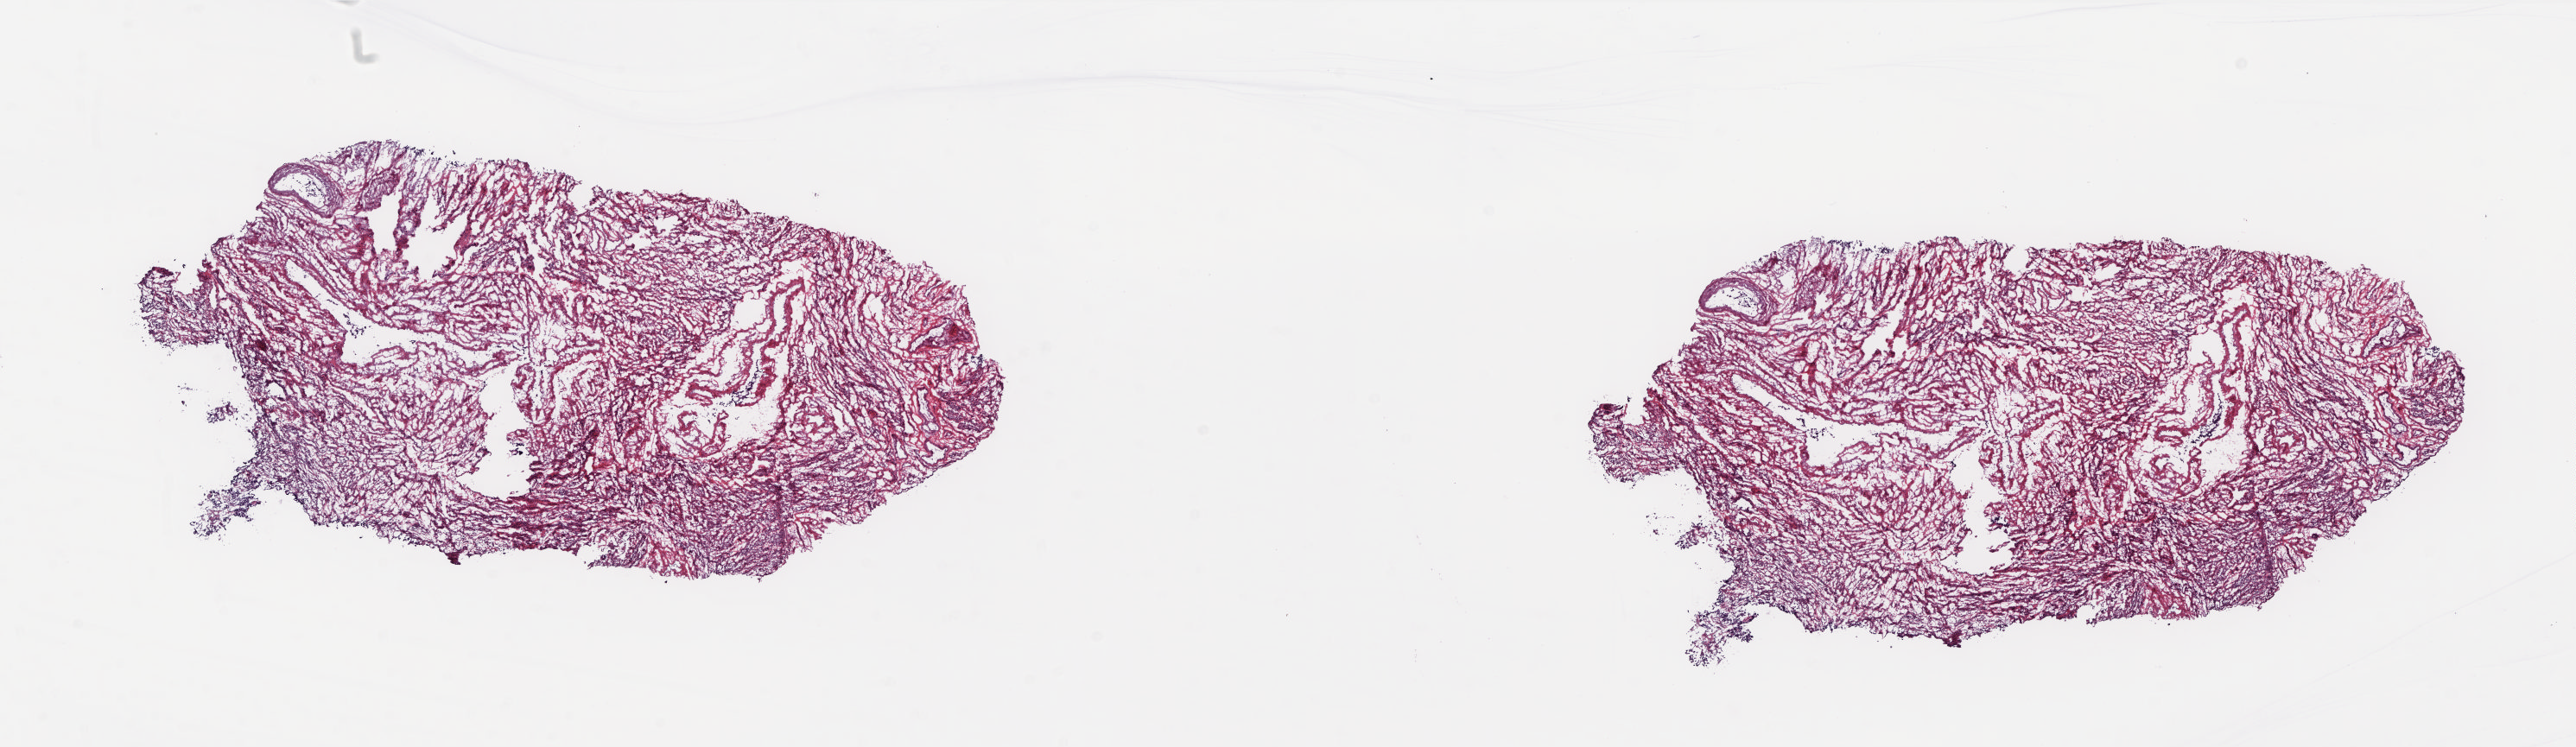
Digitized H&E-stained tissue section (whole slide) — whole scanned area (about 24.0 x 7.0 mm, from a 20x scan) shown as a low-resolution overview. Frozen section from the top of the tissue portion. Uterus, solid tissue normal (non-tumour tissue) sample. Female patient; age at initial diagnosis 68 years. Pathologist review of this section (percent, as recorded): tumour cells 0%, tumour nuclei 0%, normal cells 100%, stromal cells 0%, necrosis 0%. Infiltration values recorded for this section: lymphocyte infiltration 0%, monocyte infiltration 0%, neutrophil infiltration 0%.
* this section: solid tissue normal sample (biorepository sample class)
* patient diagnosis: Mullerian mixed tumor